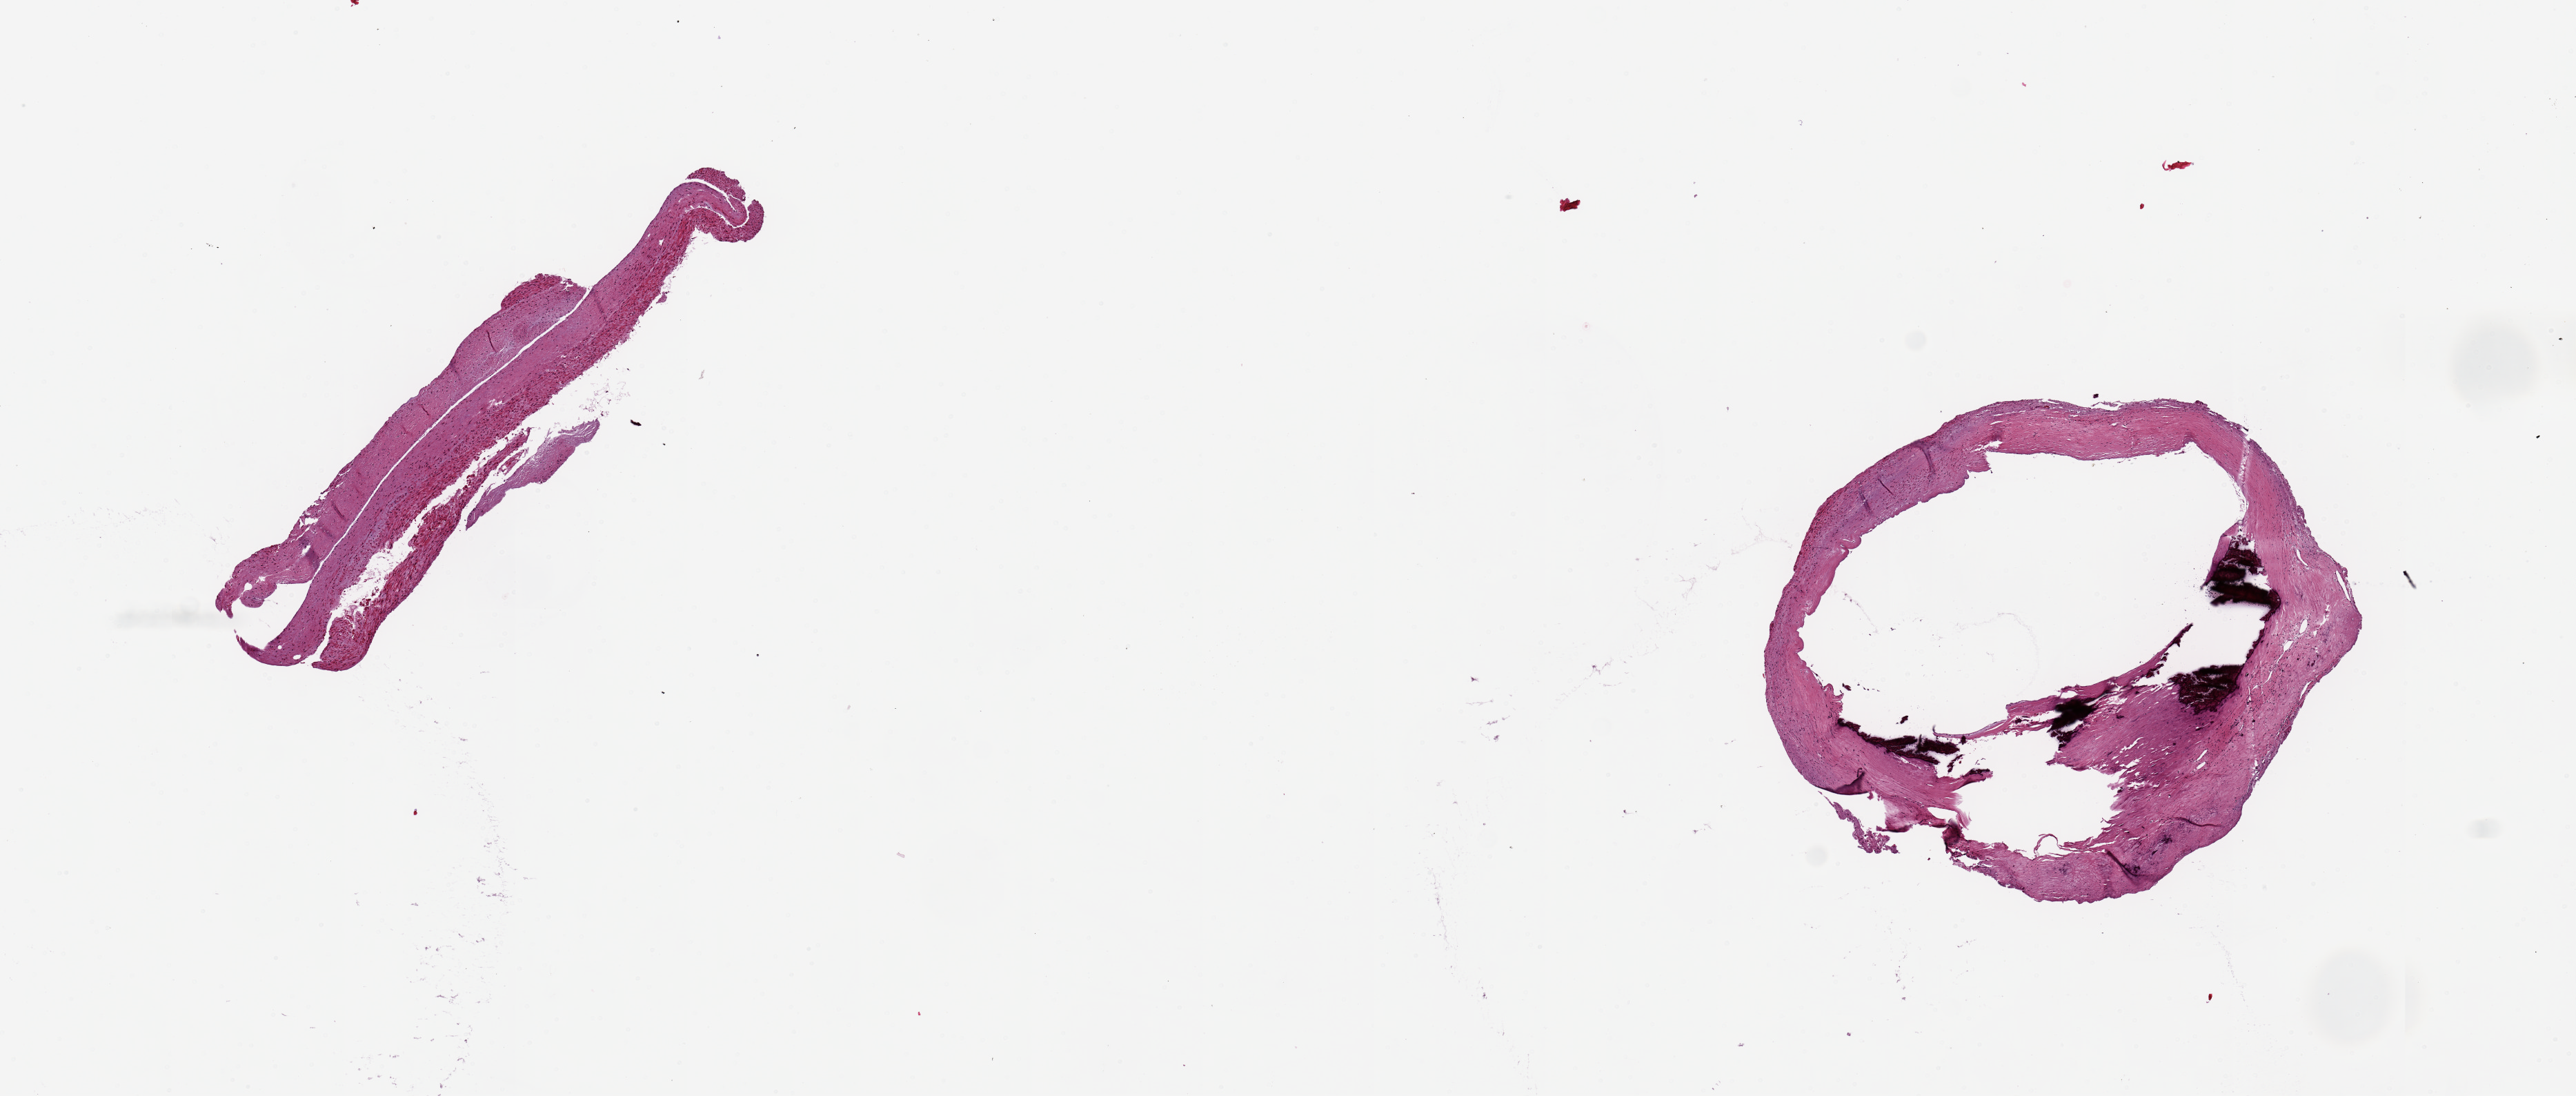
Digitized haematoxylin and eosin-stained section, brightfield — whole scanned area (about 14.8 x 6.3 mm, slide scanned at 20x) shown as a low-resolution overview, PAXgene-fixed, paraffin-embedded tissue, target tissue: coronary artery, donor tissue sample. Male donor.
Reviewer comment on this tissue sample: 2 pieces, 4mmx1m & 3x3mm; 1 with fibrocalcific plaque; history of coronary artery bypass graft.